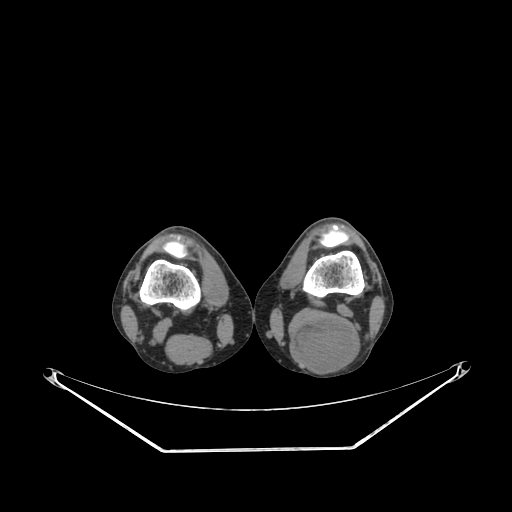
CT of an extremity soft-tissue mass (from a PET/CT study), one axial slice. Position 187 of 267 along the scan axis. 140 kVp. Soft-tissue window (W 400 / L 40 HU). 3.75 mm slice thickness. 512 × 512 image matrix. Male patient. From the clinical record (not read from this slice): histological type: synovial sarcoma; site of the primary tumour: left poplietal fossa.
Annotated regions visible in this slice (expert contour drawn on MRI and transferred to this co-registered scan by the dataset authors):
- gross tumour volume (mass): box from (x=290, y=315) to (x=362, y=373) px